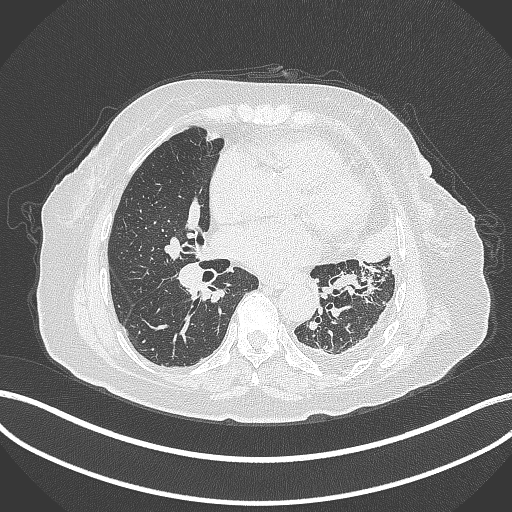
Chest CT, one axial slice. Position 172 of 399 along the scan axis. Lung window (W 1500 / L -600 HU). 1 mm slice thickness. 512 × 512 image matrix, field of view 400 × 400 mm. Female patient, age 75 years. From the clinical record (not read from this slice): clinical TNM (as recorded): T3 N3 M1.
Outlined on this slice (rectangle marked by the reading radiologist):
- lung tumour (recorded histology: adenocarcinoma): bounding box <355,215,405,271> (left, top, right, bottom; pixels)